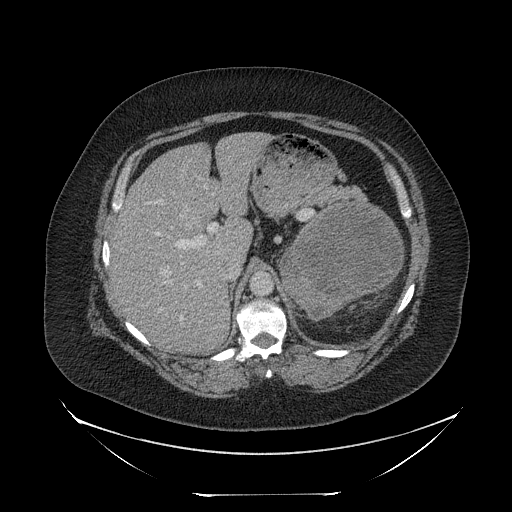
Contrast-enhanced abdominal CT, one axial slice. Slice 158 of 205 in the series (ordered by position). 120 kVp. Intravenous contrast given. Soft-tissue window (W 400 / L 40 HU). 512 × 512 image matrix, field of view 500 × 500 mm. Patient: female, 53 years. Case-level facts recorded for this patient, not image findings: diagnosis: adrenocortical carcinoma; tumour side: left adrenal; tumour size at pathology: 17 cm; Ki-67 index: 20 %; stage (as recorded): 3.
Annotated regions visible in this slice (semi-automatic segmentation, software-assisted and operator-edited):
- mass: bounding box [x1, y1, x2, y2] px = [281, 203, 401, 316]